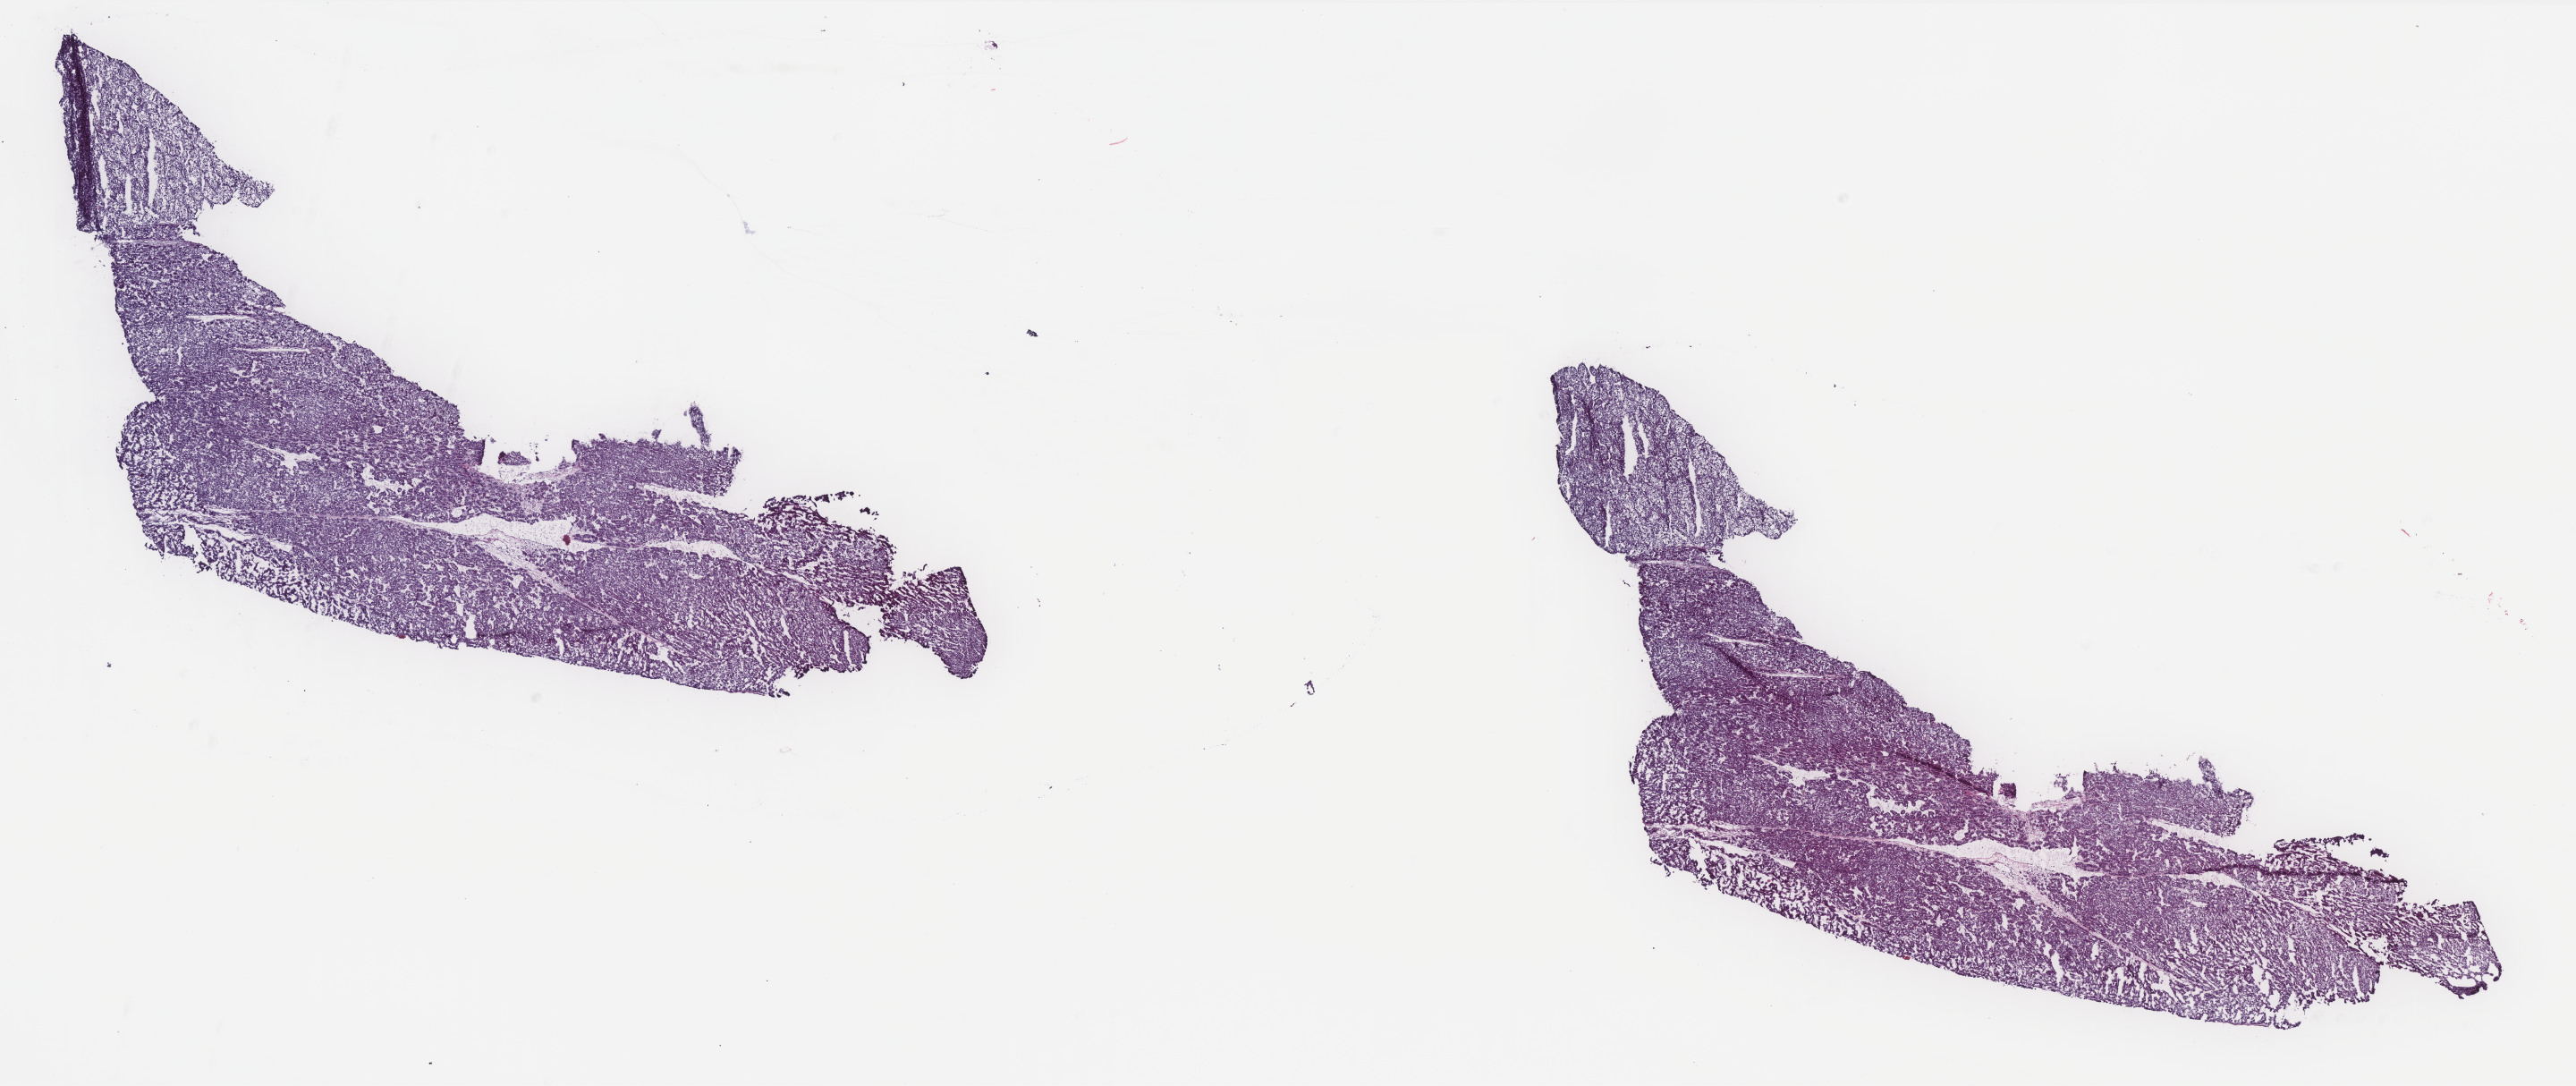
Digitized H&E-stained tissue section (whole slide), low-resolution overview of the scanned area, about 23.1 x 9.7 mm. Frozen section from the top of the tissue portion. Sample: primary tumour, liver. Female, age 72 years at initial diagnosis. Histologic grade: G2 (moderately differentiated). Composition of this section per pathologist review: tumour cells 100%, tumour nuclei 95%, normal cells 0%, stromal cells 0%, necrosis 0%. Infiltration values recorded for this section: lymphocyte infiltration 0%, monocyte infiltration 0%, neutrophil infiltration 0%.
- pathologic diagnosis: Hepatocellular carcinoma, NOS
- TNM: T1 N0 M0
- AJCC pathologic stage: I (5th edition)